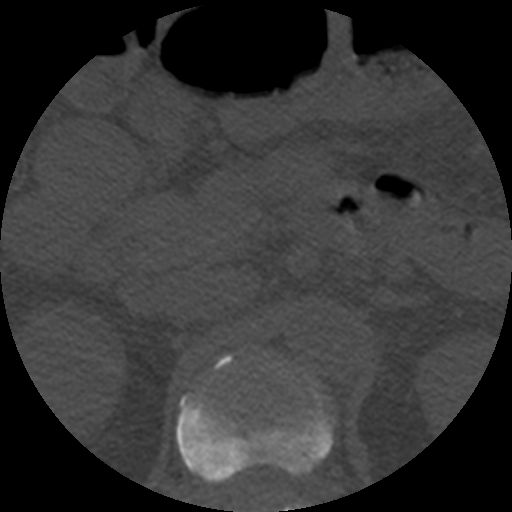
CT including the spine, one axial slice; position 203 of 508 along the scan axis; reconstruction kernel STANDARD; 120 kVp; bone window (W 1800 / L 400 HU); 1.25 mm slice thickness; 512 × 512 image matrix, field of view 160 × 160 mm. Patient age 57 years. Case-level facts recorded for this patient, not image findings: primary cancer: prostate.
Outlined on this slice (semi-automatically segmented with operator editing):
- L1 vertebra: bounding box (x1, y1, x2, y2) in pixels: (295, 503, 305, 512)
- T12 vertebra: (177, 357, 334, 484)